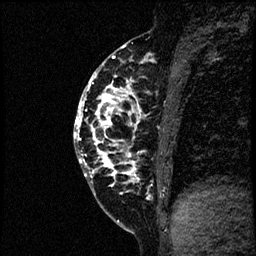
Breast MRI (dynamic contrast-enhanced), one sagittal slice; position 26 of 60 along the scan axis; dynamic contrast-enhanced study with each time point stored as its own series, time point 2 of 4 at this slice position (early post-contrast, ordered by acquisition time); 1.5 T; TE 4.2 ms, TR 17.6 ms; 2 mm slice thickness; 256 × 256 image matrix, field of view 200 × 200 mm. Patient: female, 40 years. Case-level facts recorded for this patient, not image findings: setting: breast cancer imaged before/during neoadjuvant chemotherapy; receptor status: HER2-positive.
Annotated regions visible in this slice (semi-automatically segmented with operator editing):
- analysis volume of interest (the breast-tissue region the enhancement analysis was run in; not a lesion): bounding box (x1, y1, x2, y2) in pixels: (75, 56, 197, 205)
- tumour enhancement mask (voxels above the 100 % enhancement threshold inside the analysis volume of interest): (75, 56, 153, 197)